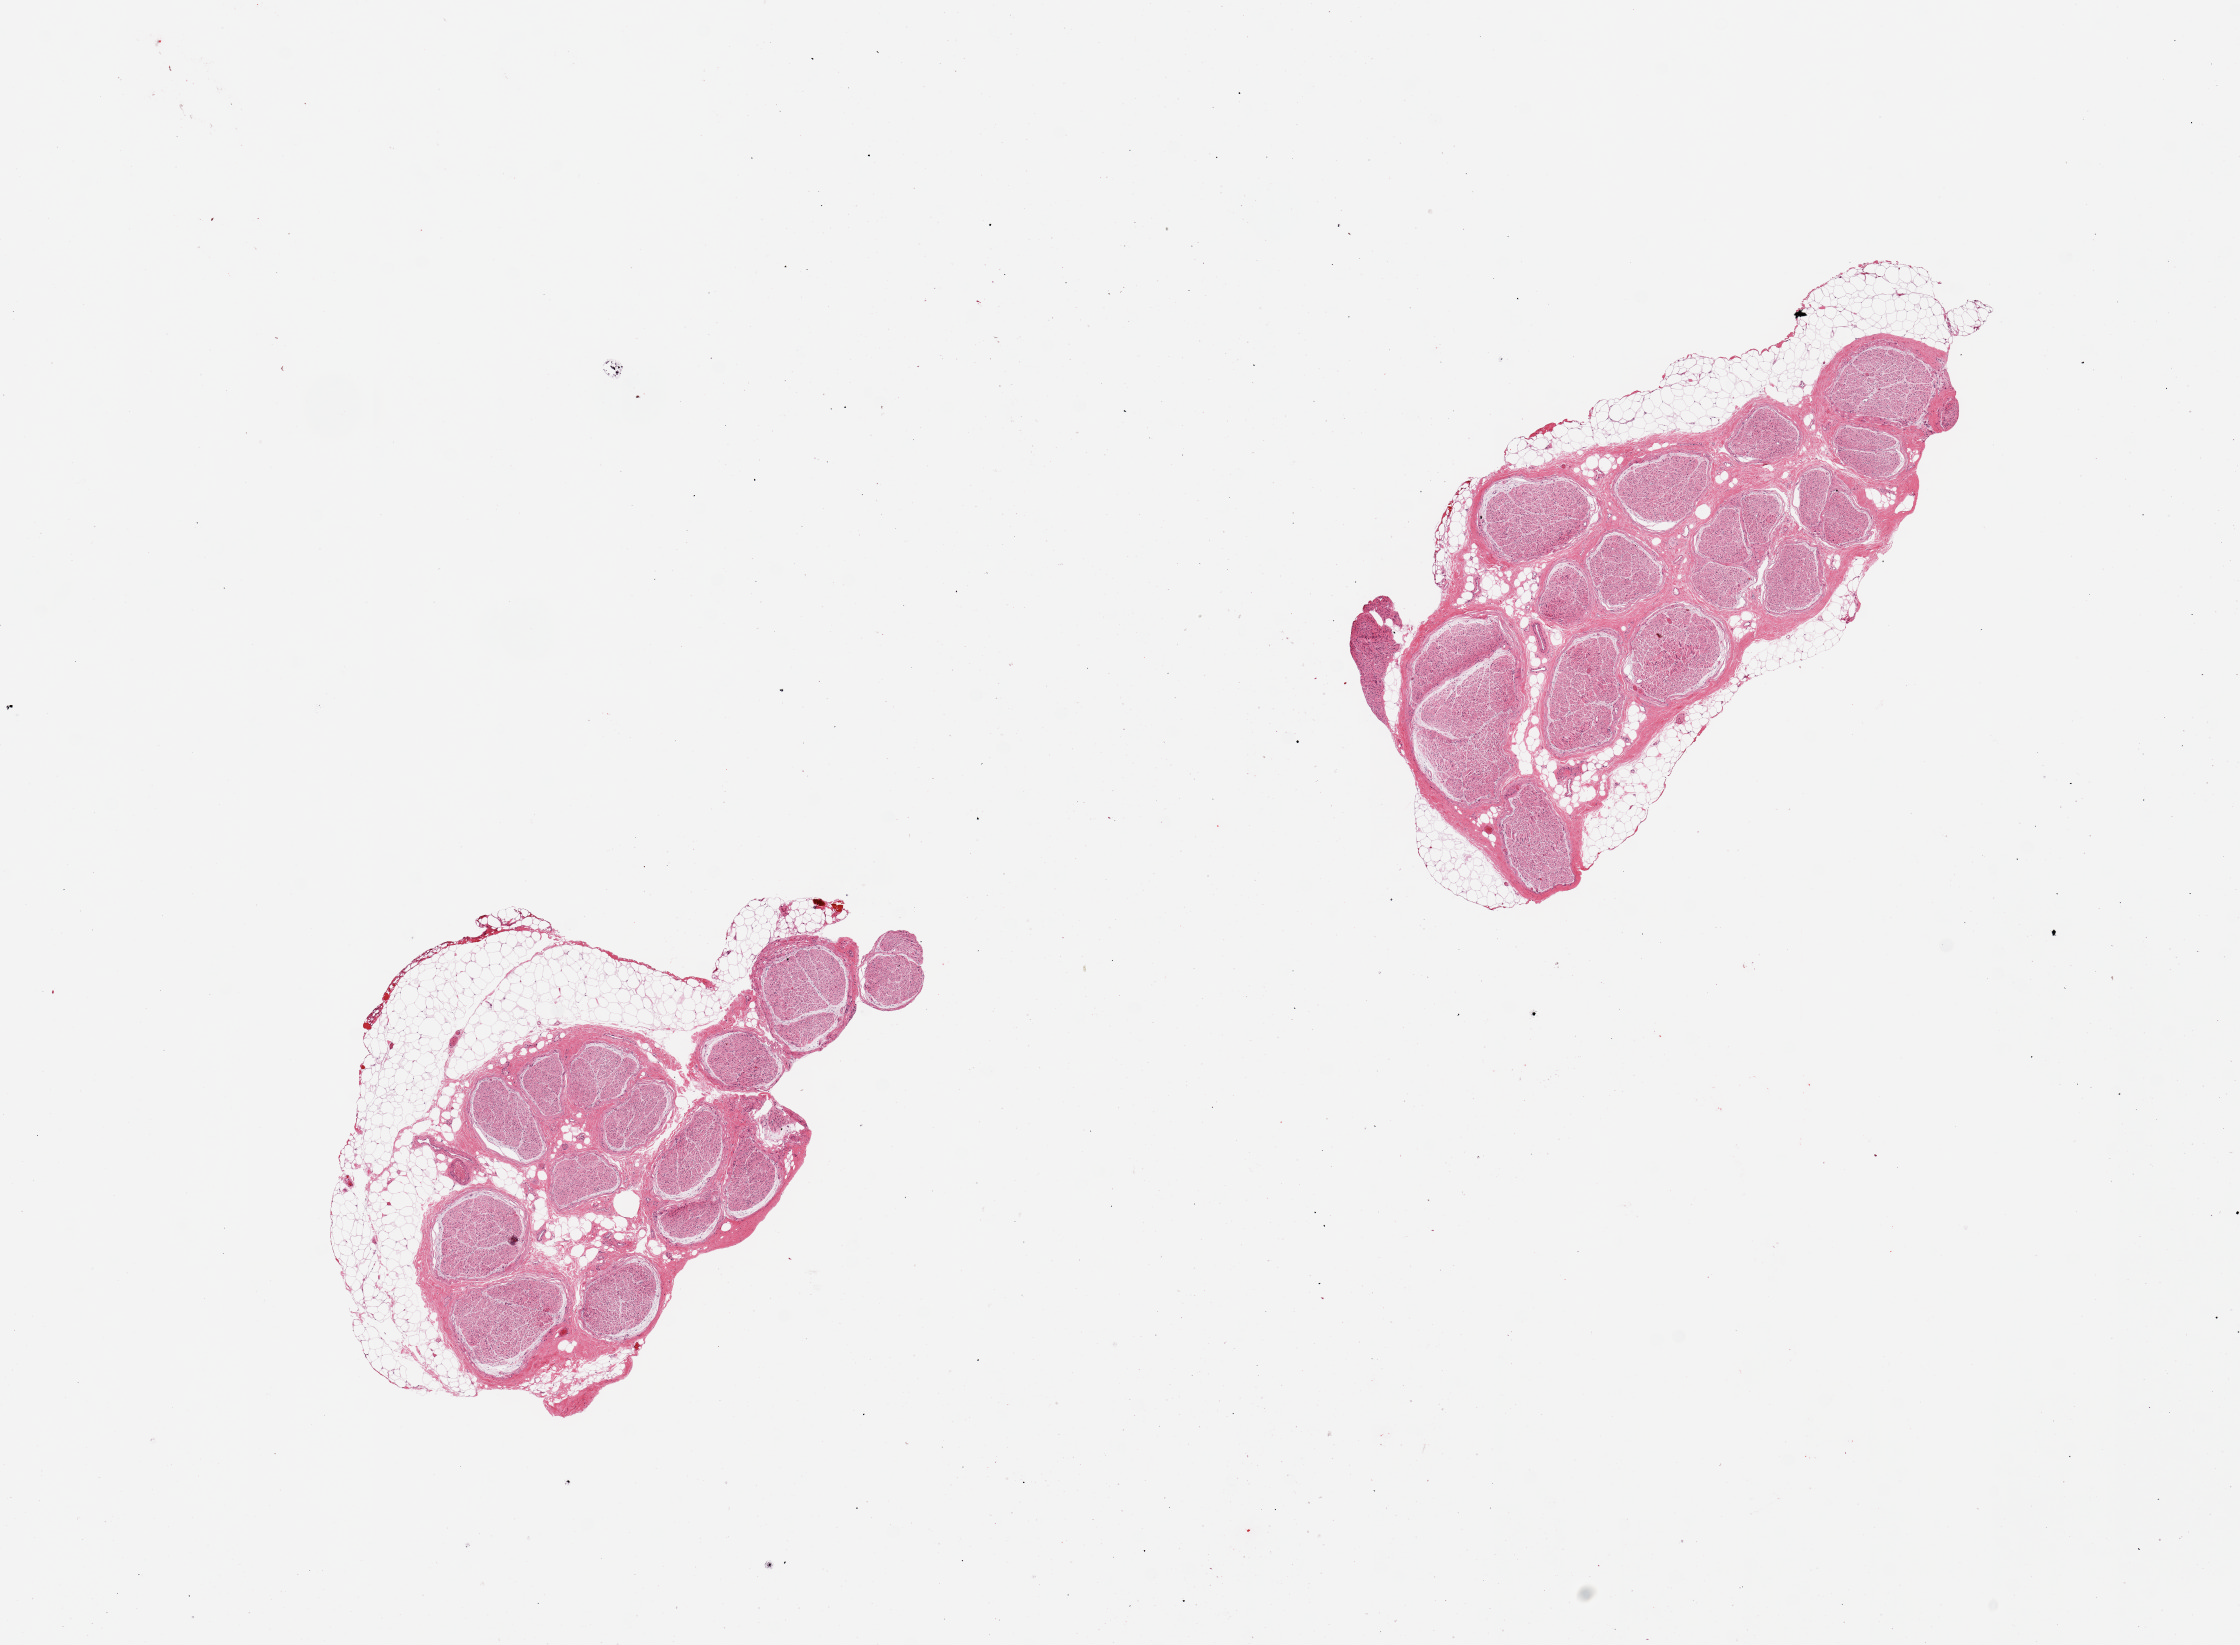
Digitized haematoxylin and eosin-stained section, brightfield — shown as a low-resolution overview of the whole scanned area (about 17.7 x 13.0 mm, slide scanned at 20x). PAXgene-fixed paraffin-embedded (PFPE) section. Sampled site (target tissue): tibial nerve. Donor tissue sample. Female donor.
- reviewer comment on this tissue sample: 2 pieces, both with partial rim of adipose tissue (~20-40% total)